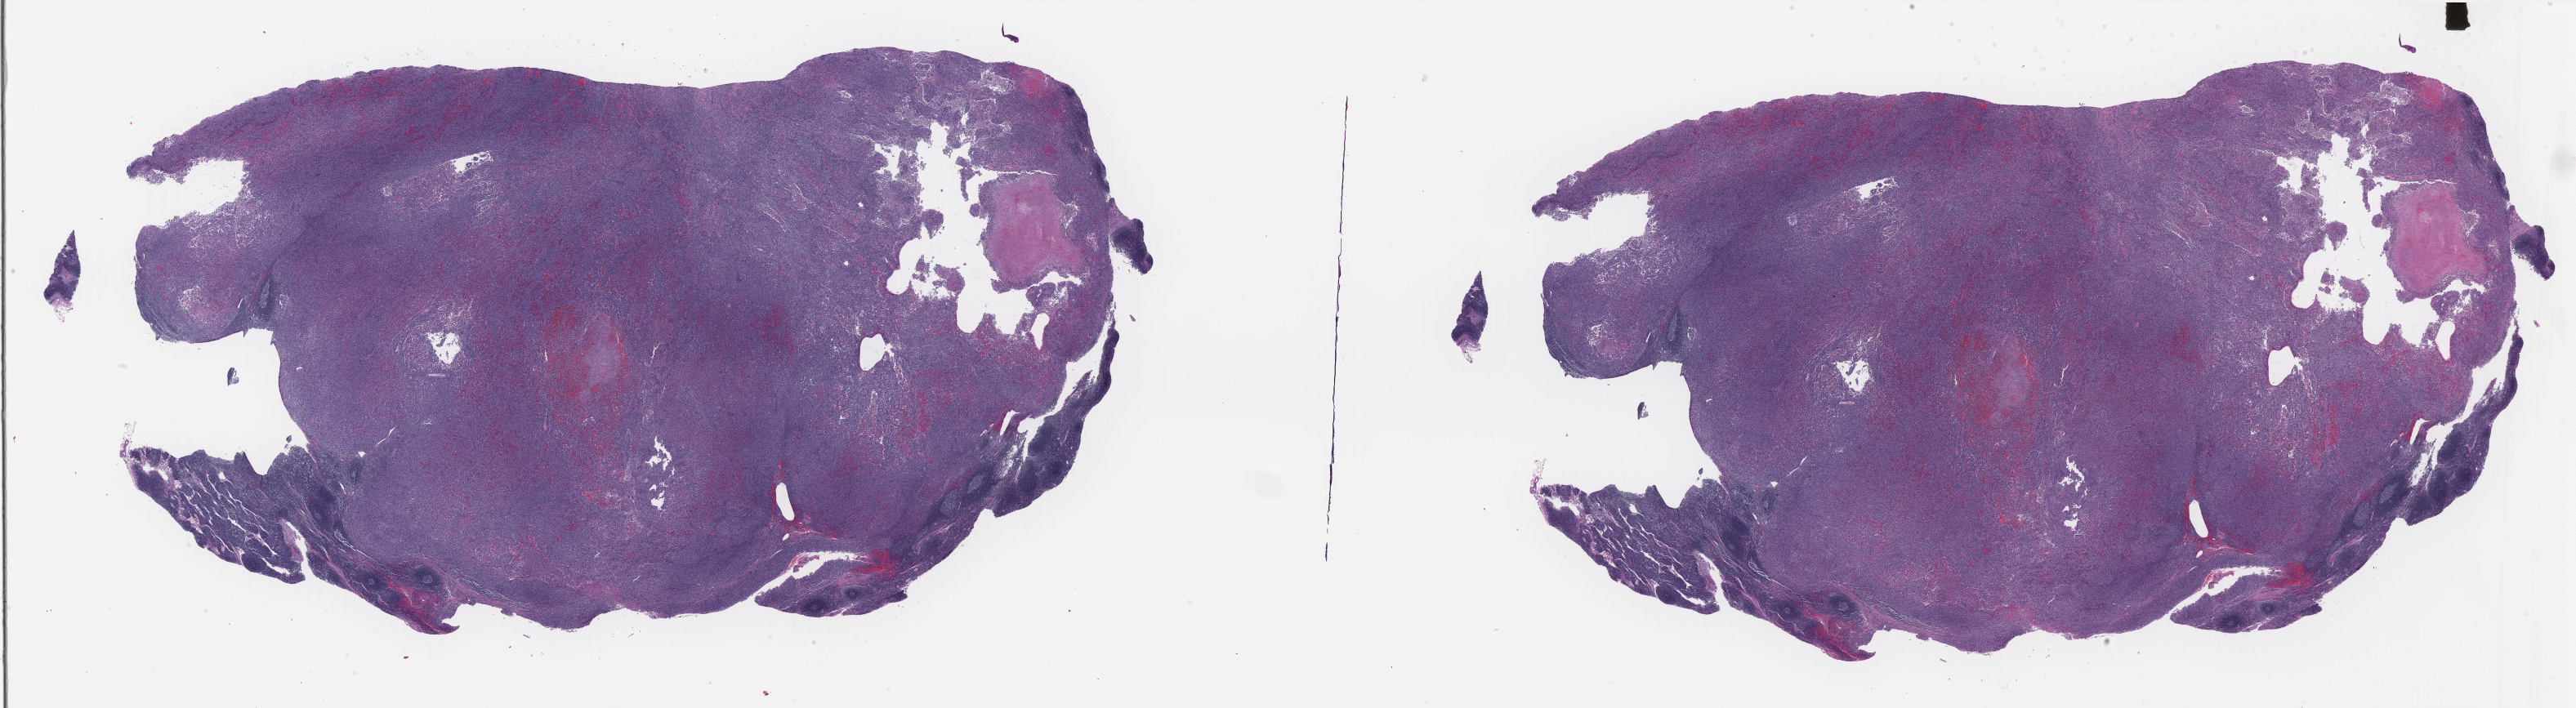
Digitized H&E-stained tissue section (whole slide), whole scanned area (about 49.9 x 13.7 mm, from a 40x scan) shown as a low-resolution overview. Formalin-fixed paraffin-embedded (FFPE) diagnostic section. Primary tumour sample from the skin. Female, age 65 years at initial diagnosis.
Histologic diagnosis: Malignant melanoma, NOS.